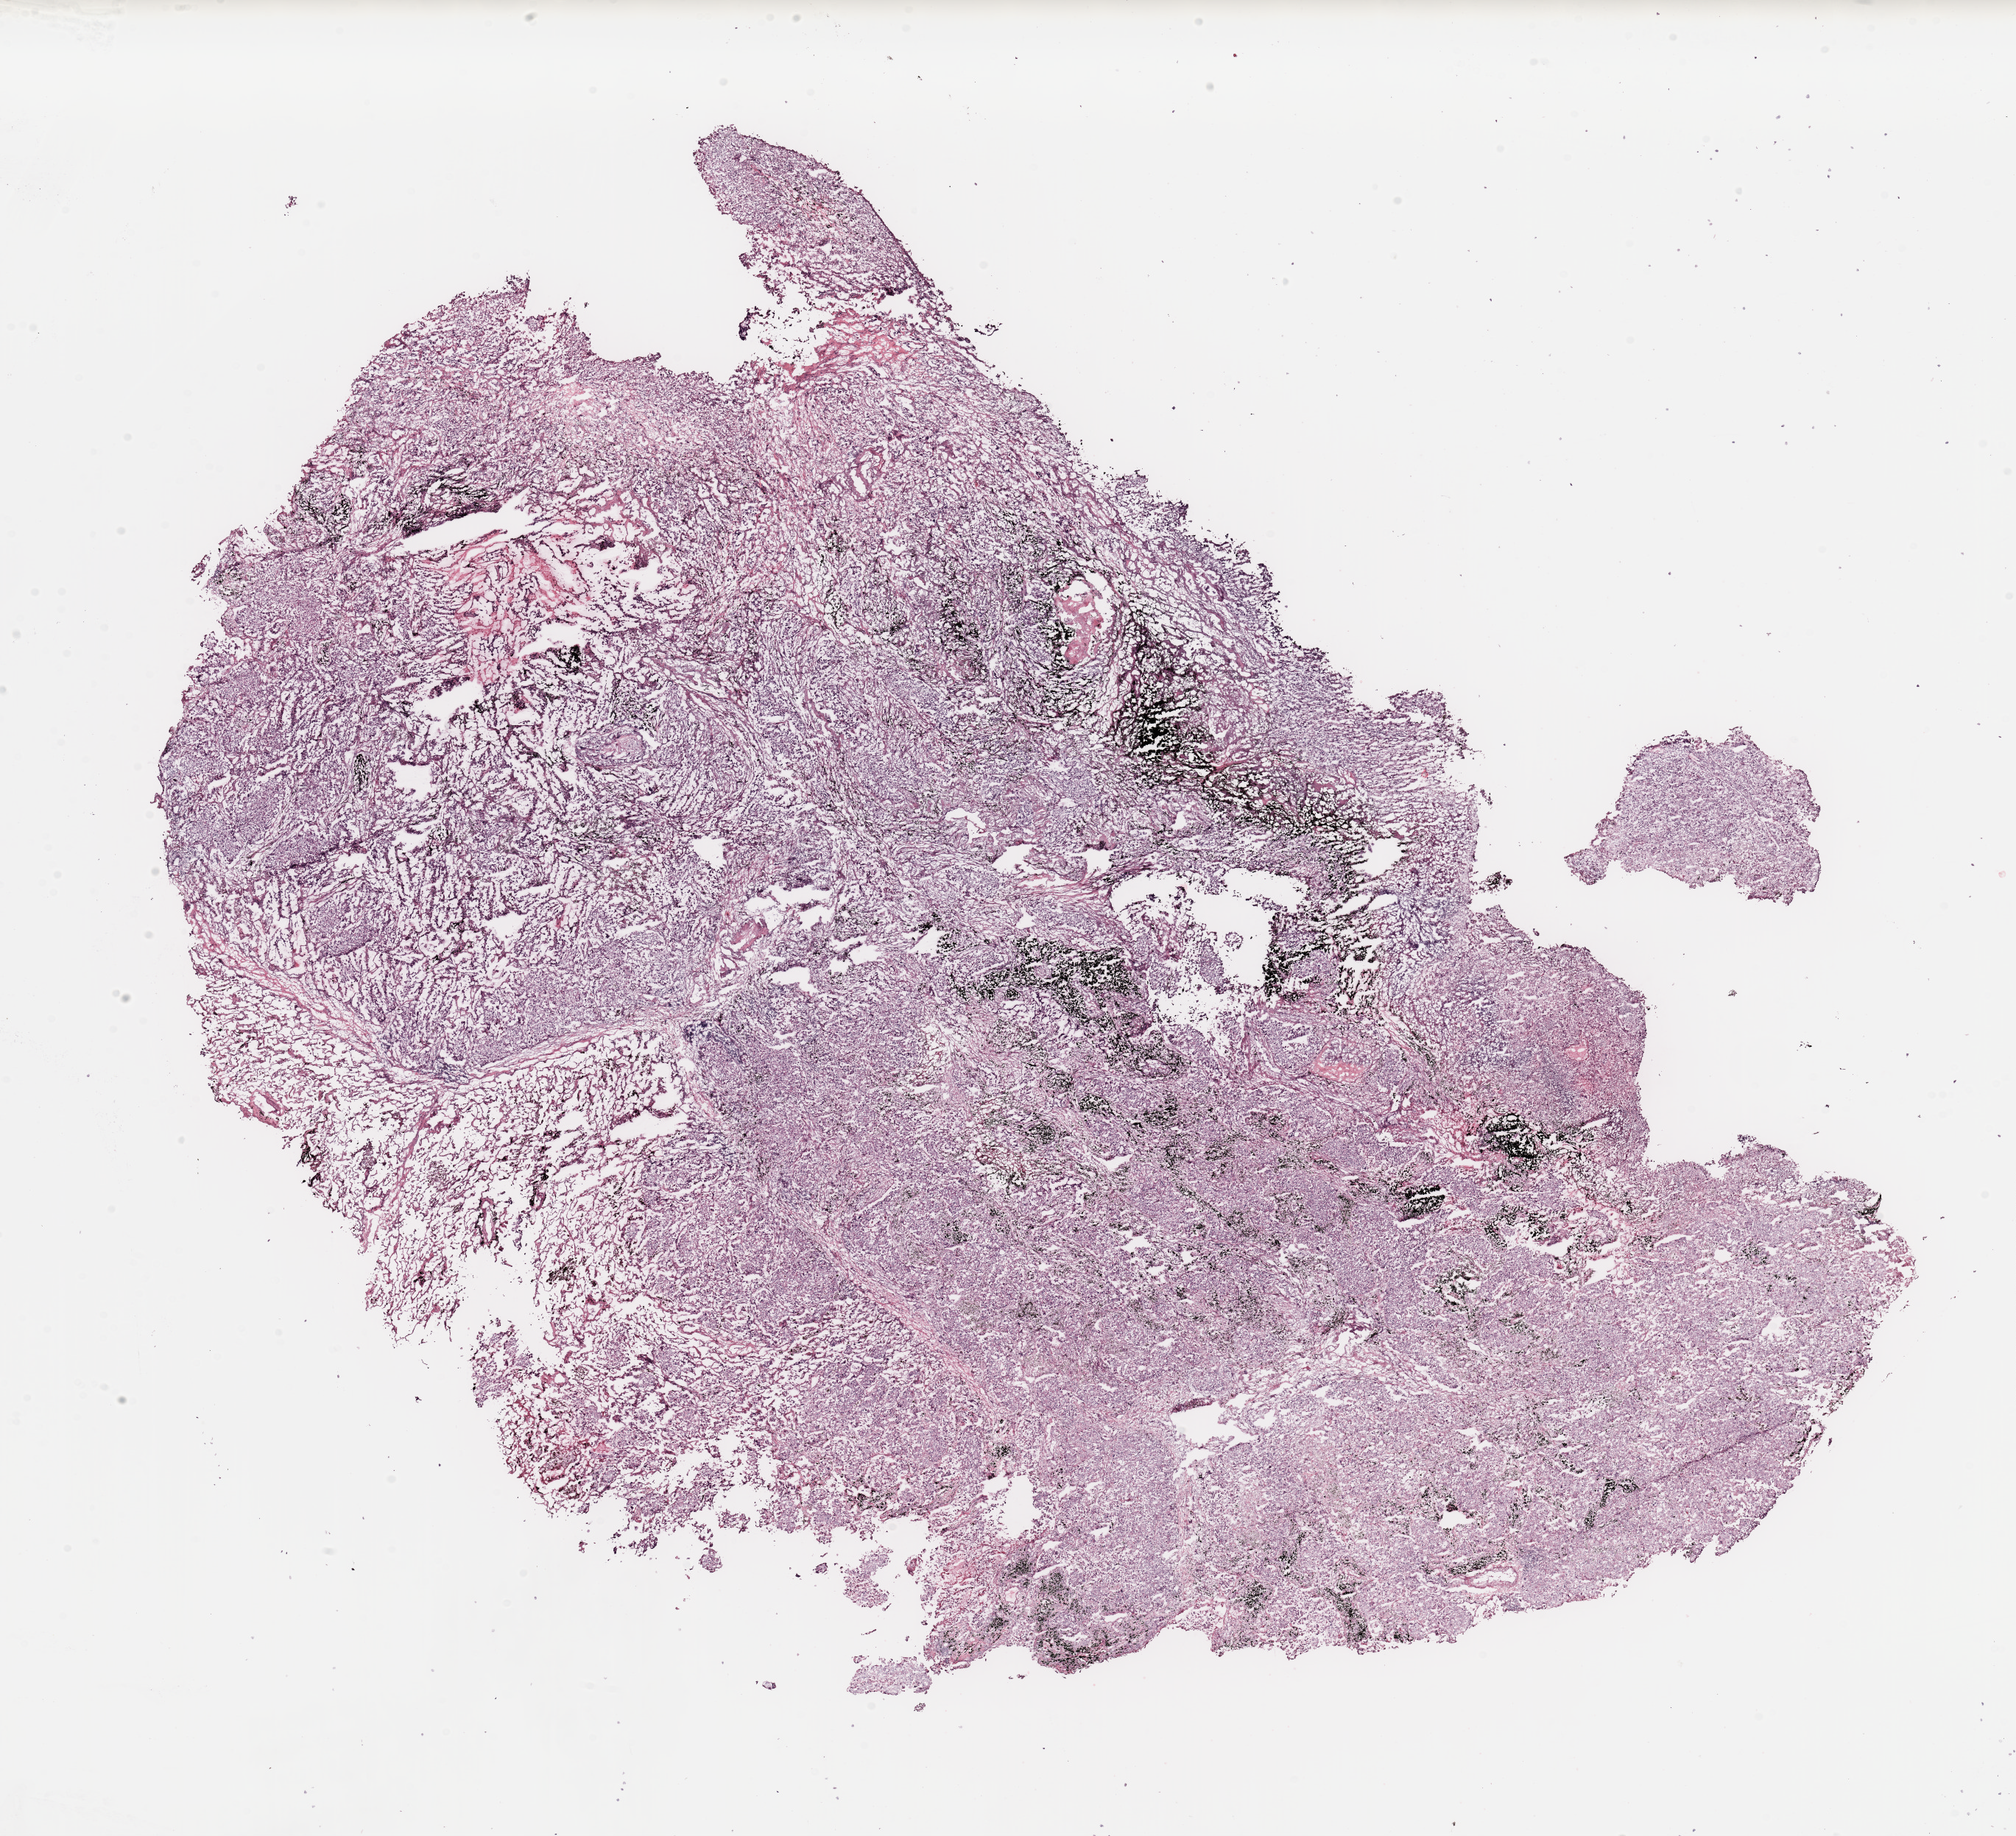
H&E whole-slide image — a low-resolution overview of the entire scanned area, about 21.7 x 19.7 mm; tumour tissue sample, sampled site: lung. Male, 59 y/o. Slide review estimates, as recorded: tumour nuclei 70%, necrosis 5%.
Histologic diagnosis: Adenocarcinoma, NOS.